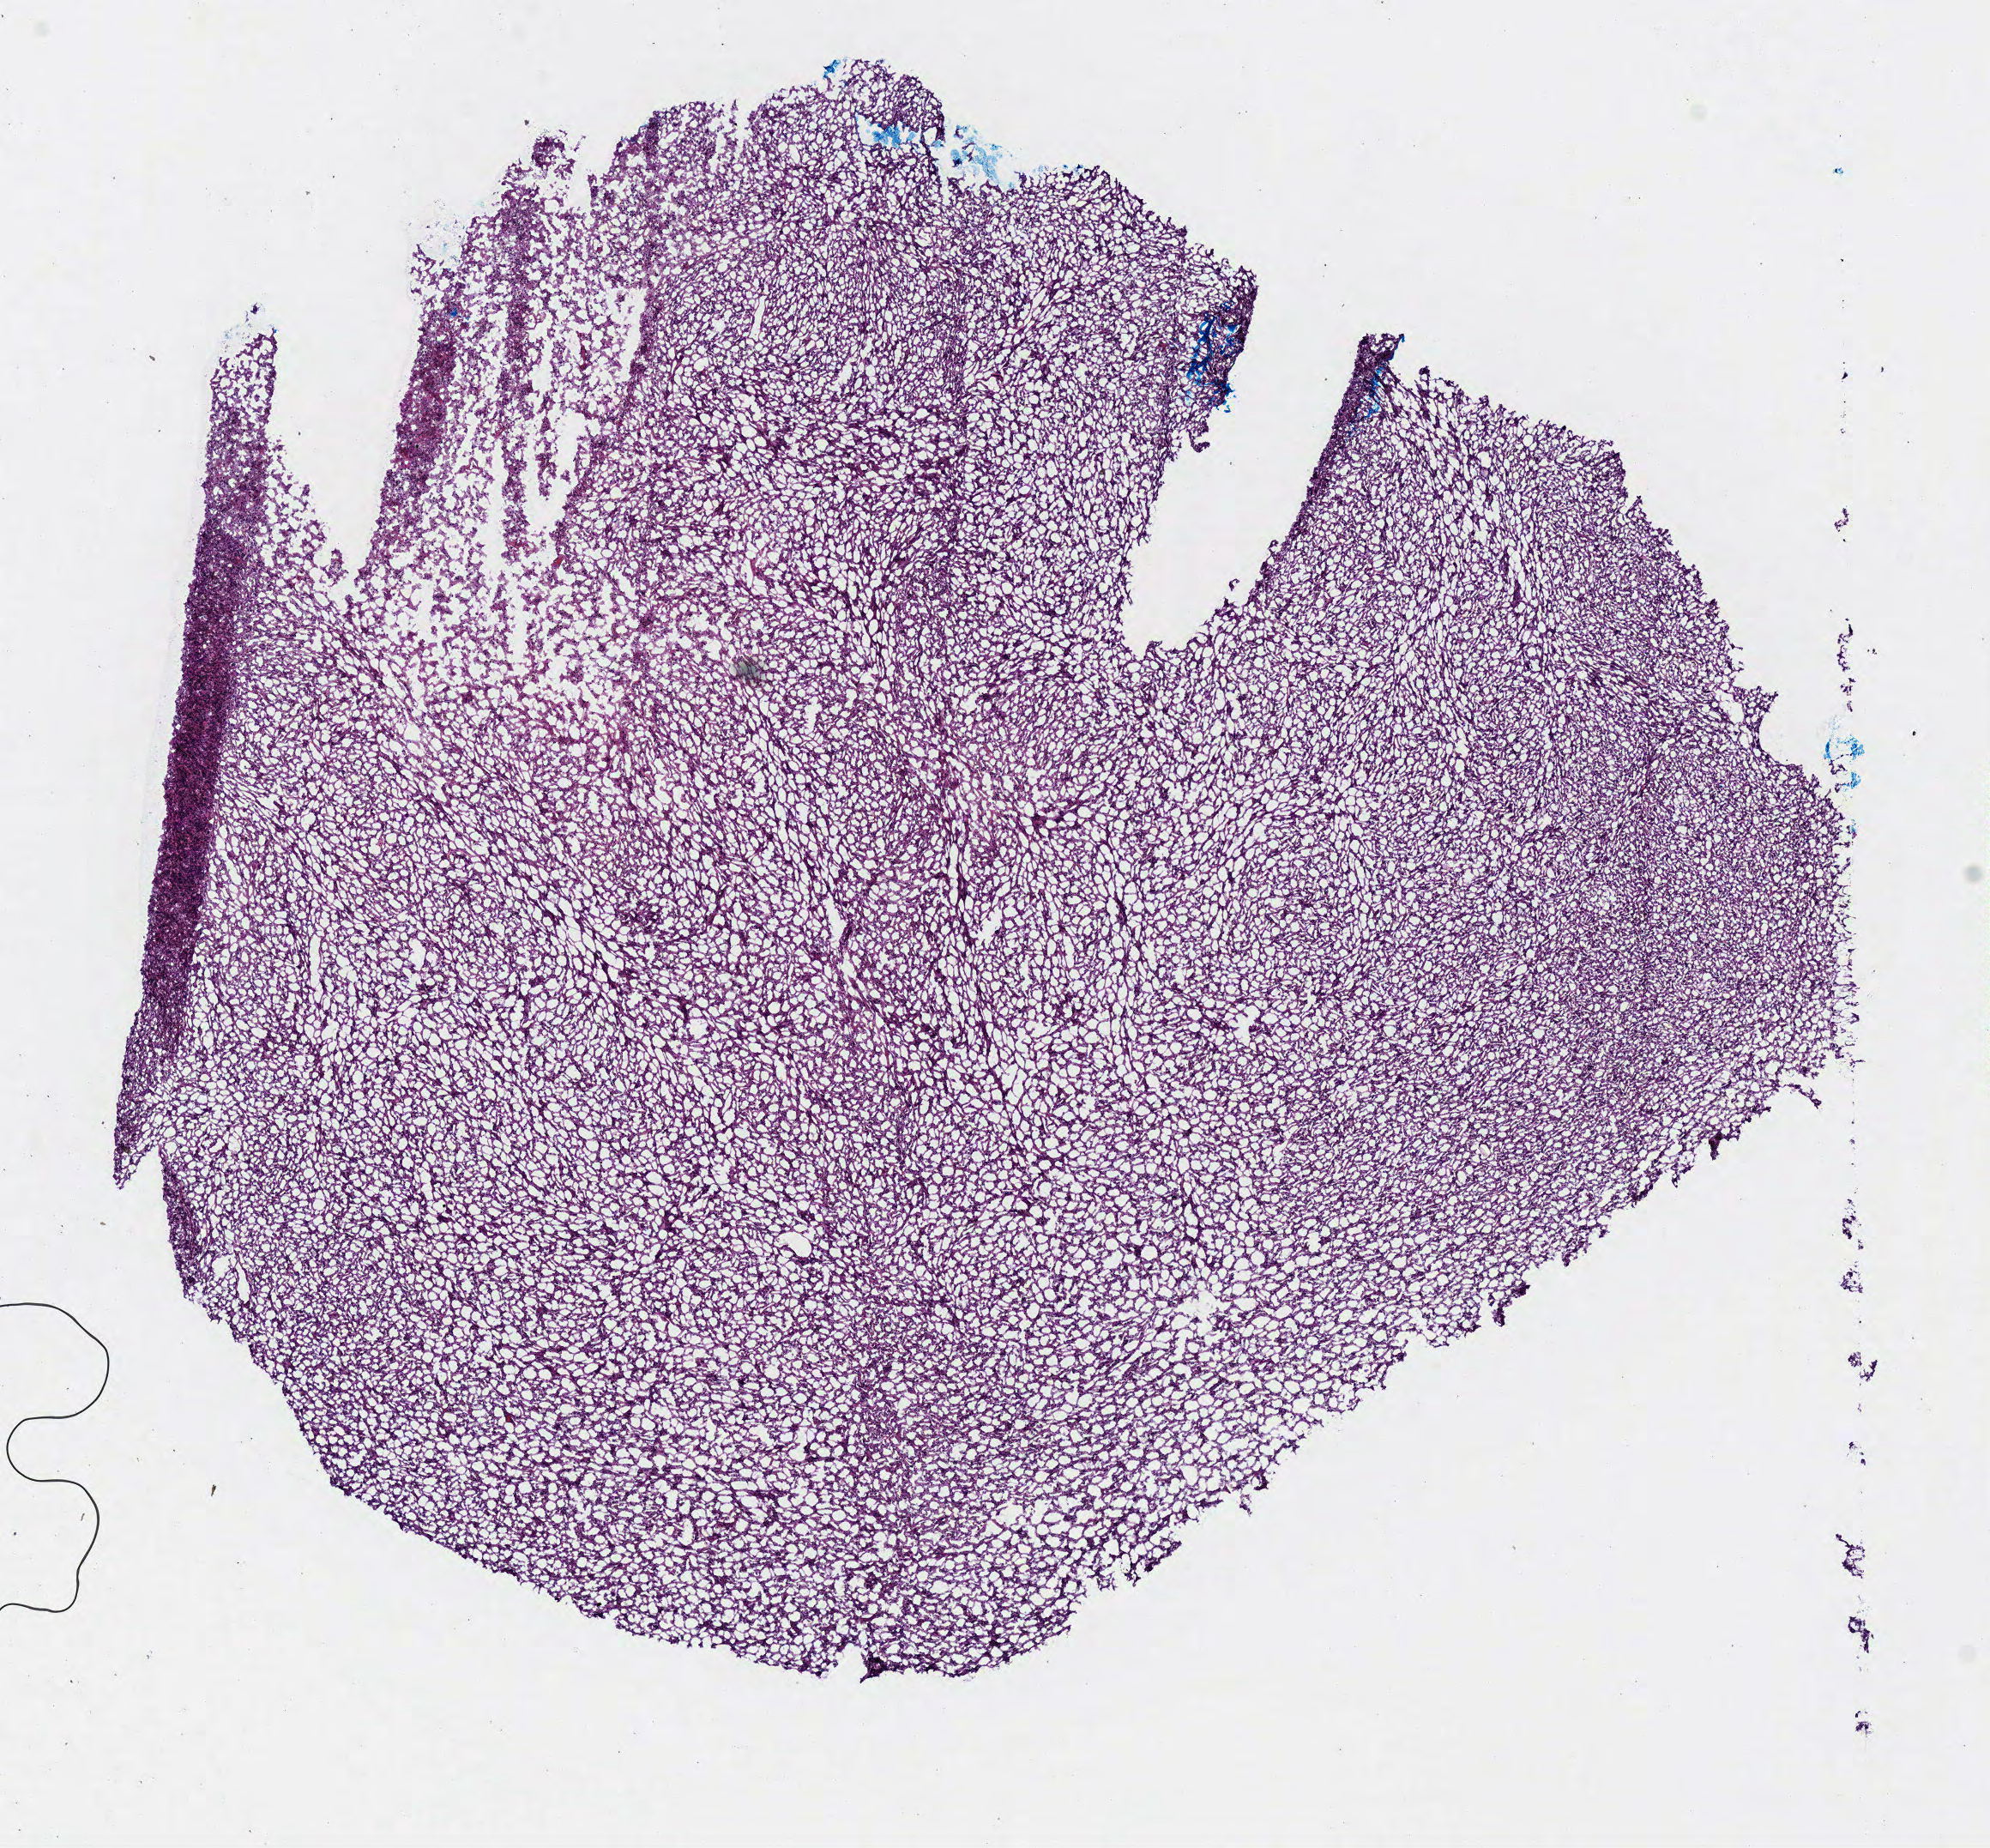
H&E-stained whole-slide image, whole scanned area (about 9.1 x 8.5 mm, slide scanned at 40x) shown as a low-resolution overview; frozen section from the bottom of the tissue portion; brain, primary tumour sample. Female, age 76 years at initial diagnosis. Pathologist review of this section (percent, as recorded): tumour cells 100%, tumour nuclei 75%, normal cells 0%, stromal cells 0%, necrosis 0%.
Diagnosis: Glioblastoma.